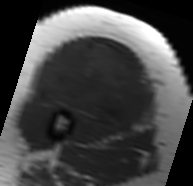
MRI of an extremity soft-tissue mass, one axial slice; slice 35 of 91 in the series (ordered by position); MR volume resampled by the dataset authors to the PET/CT grid (not the native acquisition matrix); 3.27 mm slice thickness; 193 × 186 image matrix, field of view 188 × 182 mm. Female patient. From the clinical record (not read from this slice): histological type: malignant solitary fibrous tumor; grade: intermediate; site of the primary tumour: right thigh.
Annotated regions visible in this slice (expert contour drawn on MRI and transferred to this co-registered scan by the dataset authors):
- gross tumour volume including surrounding oedema: bounding box (x1, y1, x2, y2) in pixels: (31, 39, 150, 132)
- gross tumour volume (mass): (38, 39, 148, 129)